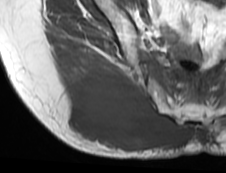
MRI of an extremity soft-tissue mass, one axial slice. Position 43 of 73 along the scan axis. MR volume resampled by the dataset authors to the PET/CT grid (not the native acquisition matrix). 3.27 mm slice thickness. 226 × 173 image matrix. Female patient. Case-level facts recorded for this patient, not image findings: histological type: spindle cell suggestive of myxofibrosarcoma; grade: intermediate; site of the primary tumour: right buttock.
Outlined on this slice (expert contour drawn on MRI and transferred to this co-registered scan by the dataset authors):
- gross tumour volume (mass): bounding box [x1, y1, x2, y2] px = [63, 69, 190, 153]